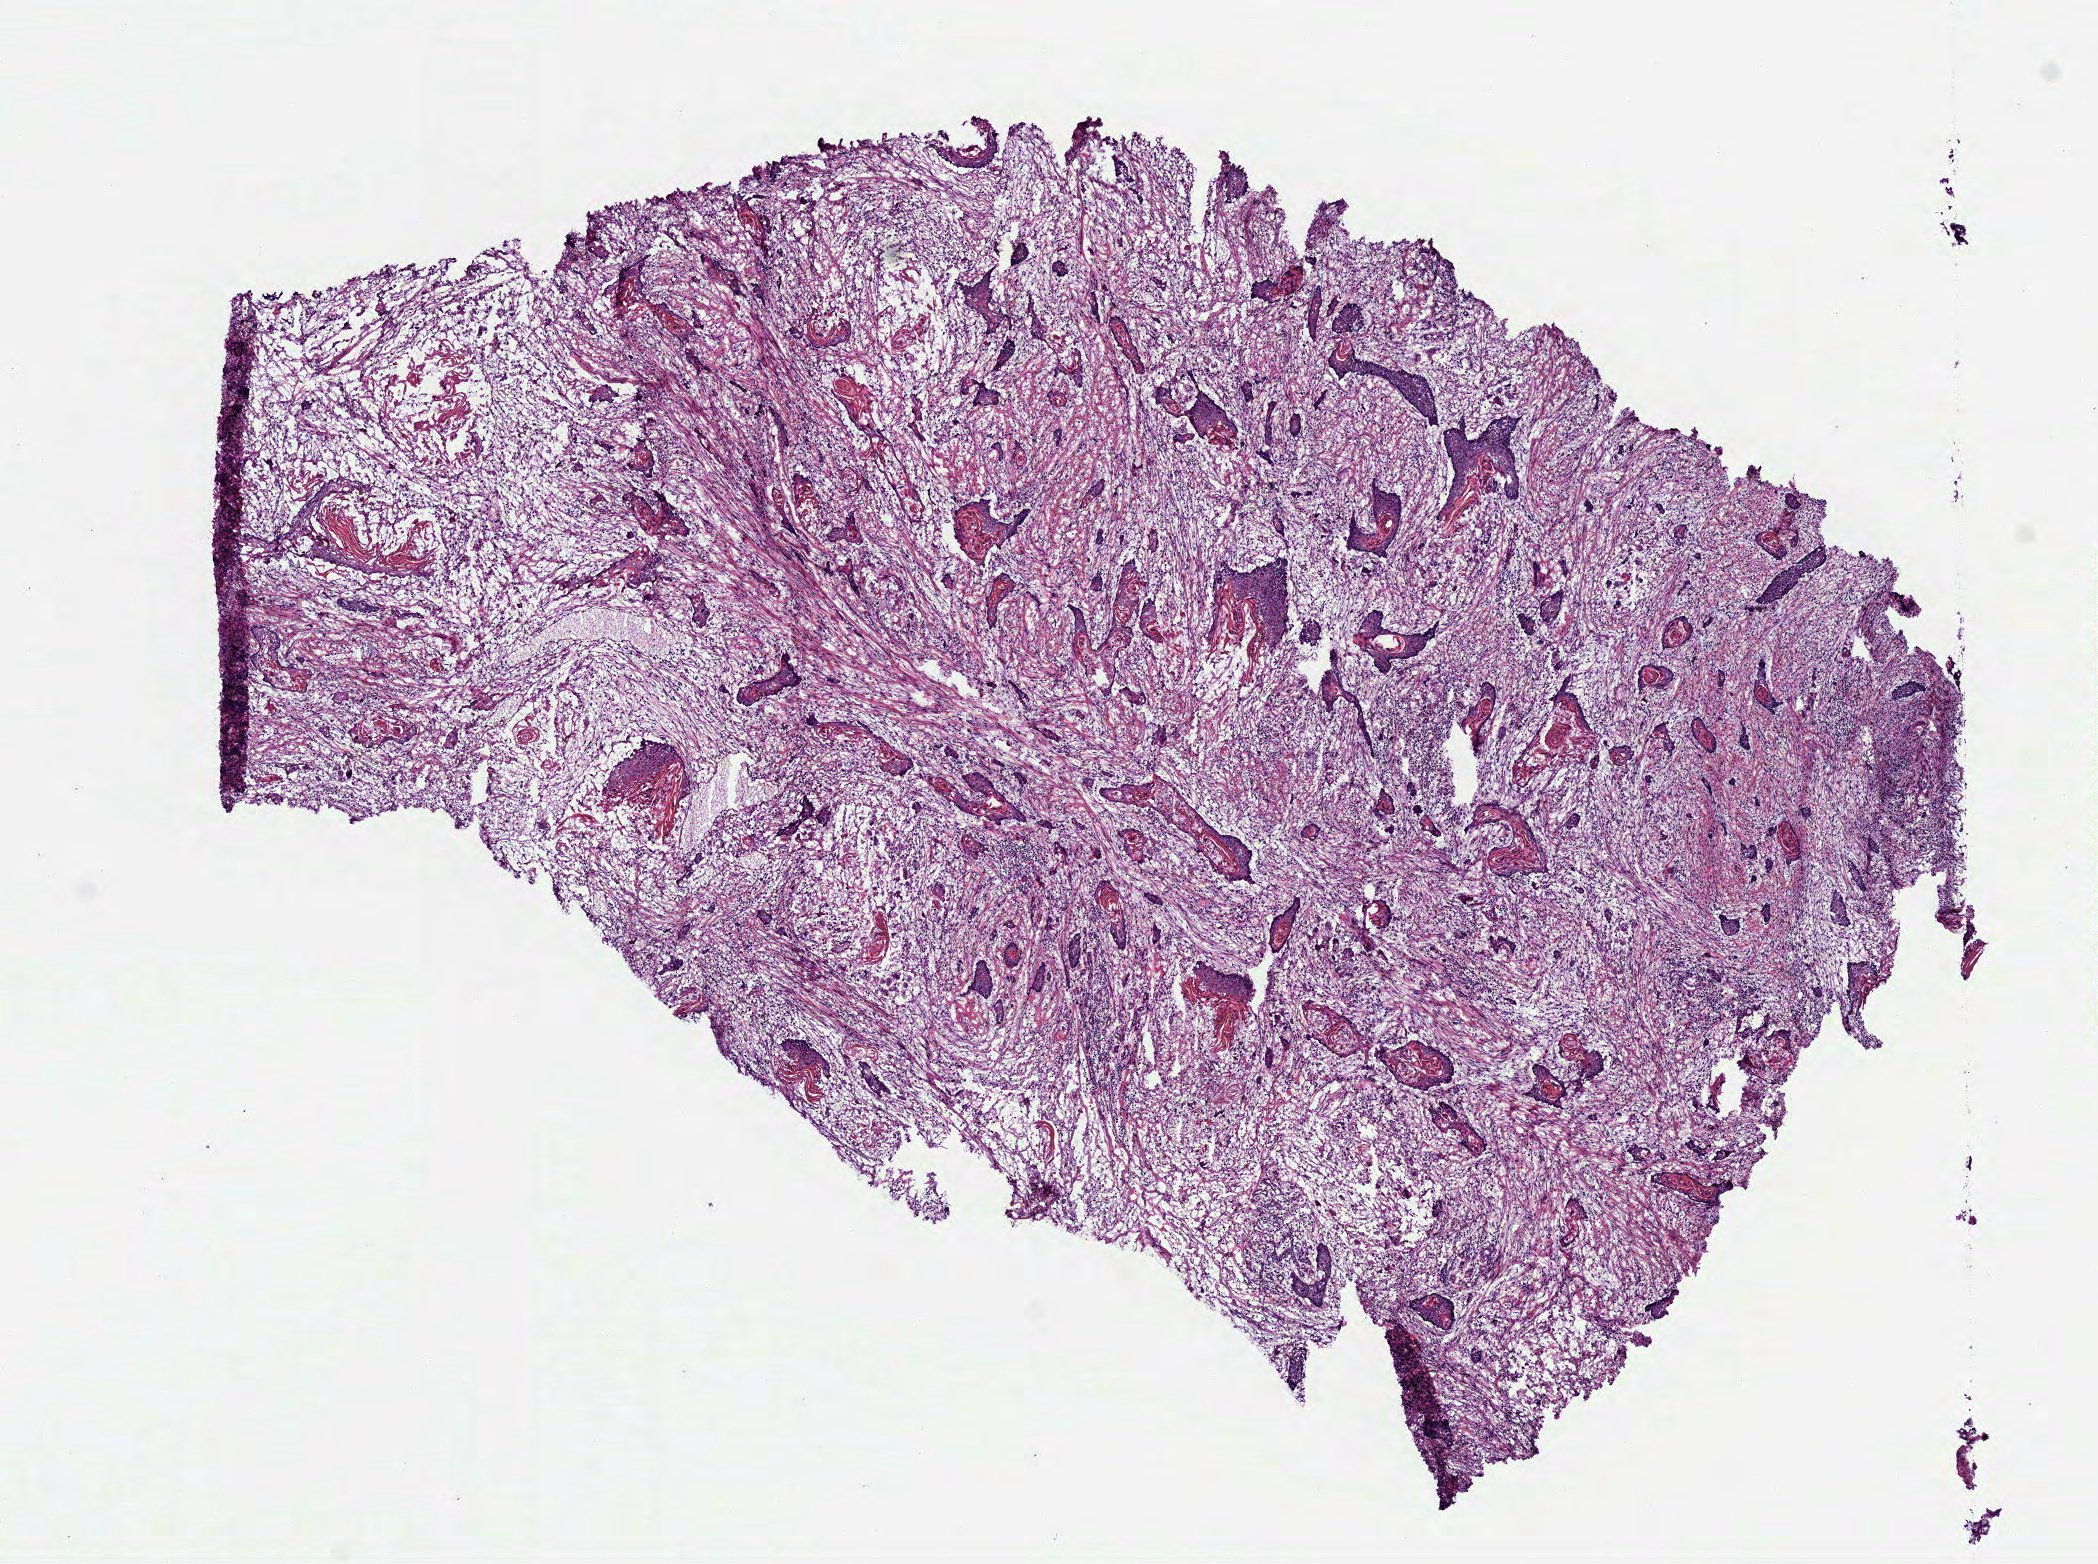
Hematoxylin and eosin (H&E) stained whole-slide image, shown as a low-resolution overview of the whole scanned area (about 8.5 x 6.3 mm, slide scanned at 40x). Frozen section from the bottom of the tissue portion. Sample: primary tumour, head and neck. Male, age 61 years at initial diagnosis. Histologic grade: G2 (moderately differentiated). Slide review estimates, as recorded: tumour cells 25%, tumour nuclei 50%, normal cells 0%, stromal cells 75%, necrosis 0%.
- lymph nodes positive (case pathology): 0 of 45 examined
- AJCC pathologic stage: IVA (7th edition)
- pathologic diagnosis: Squamous cell carcinoma, NOS